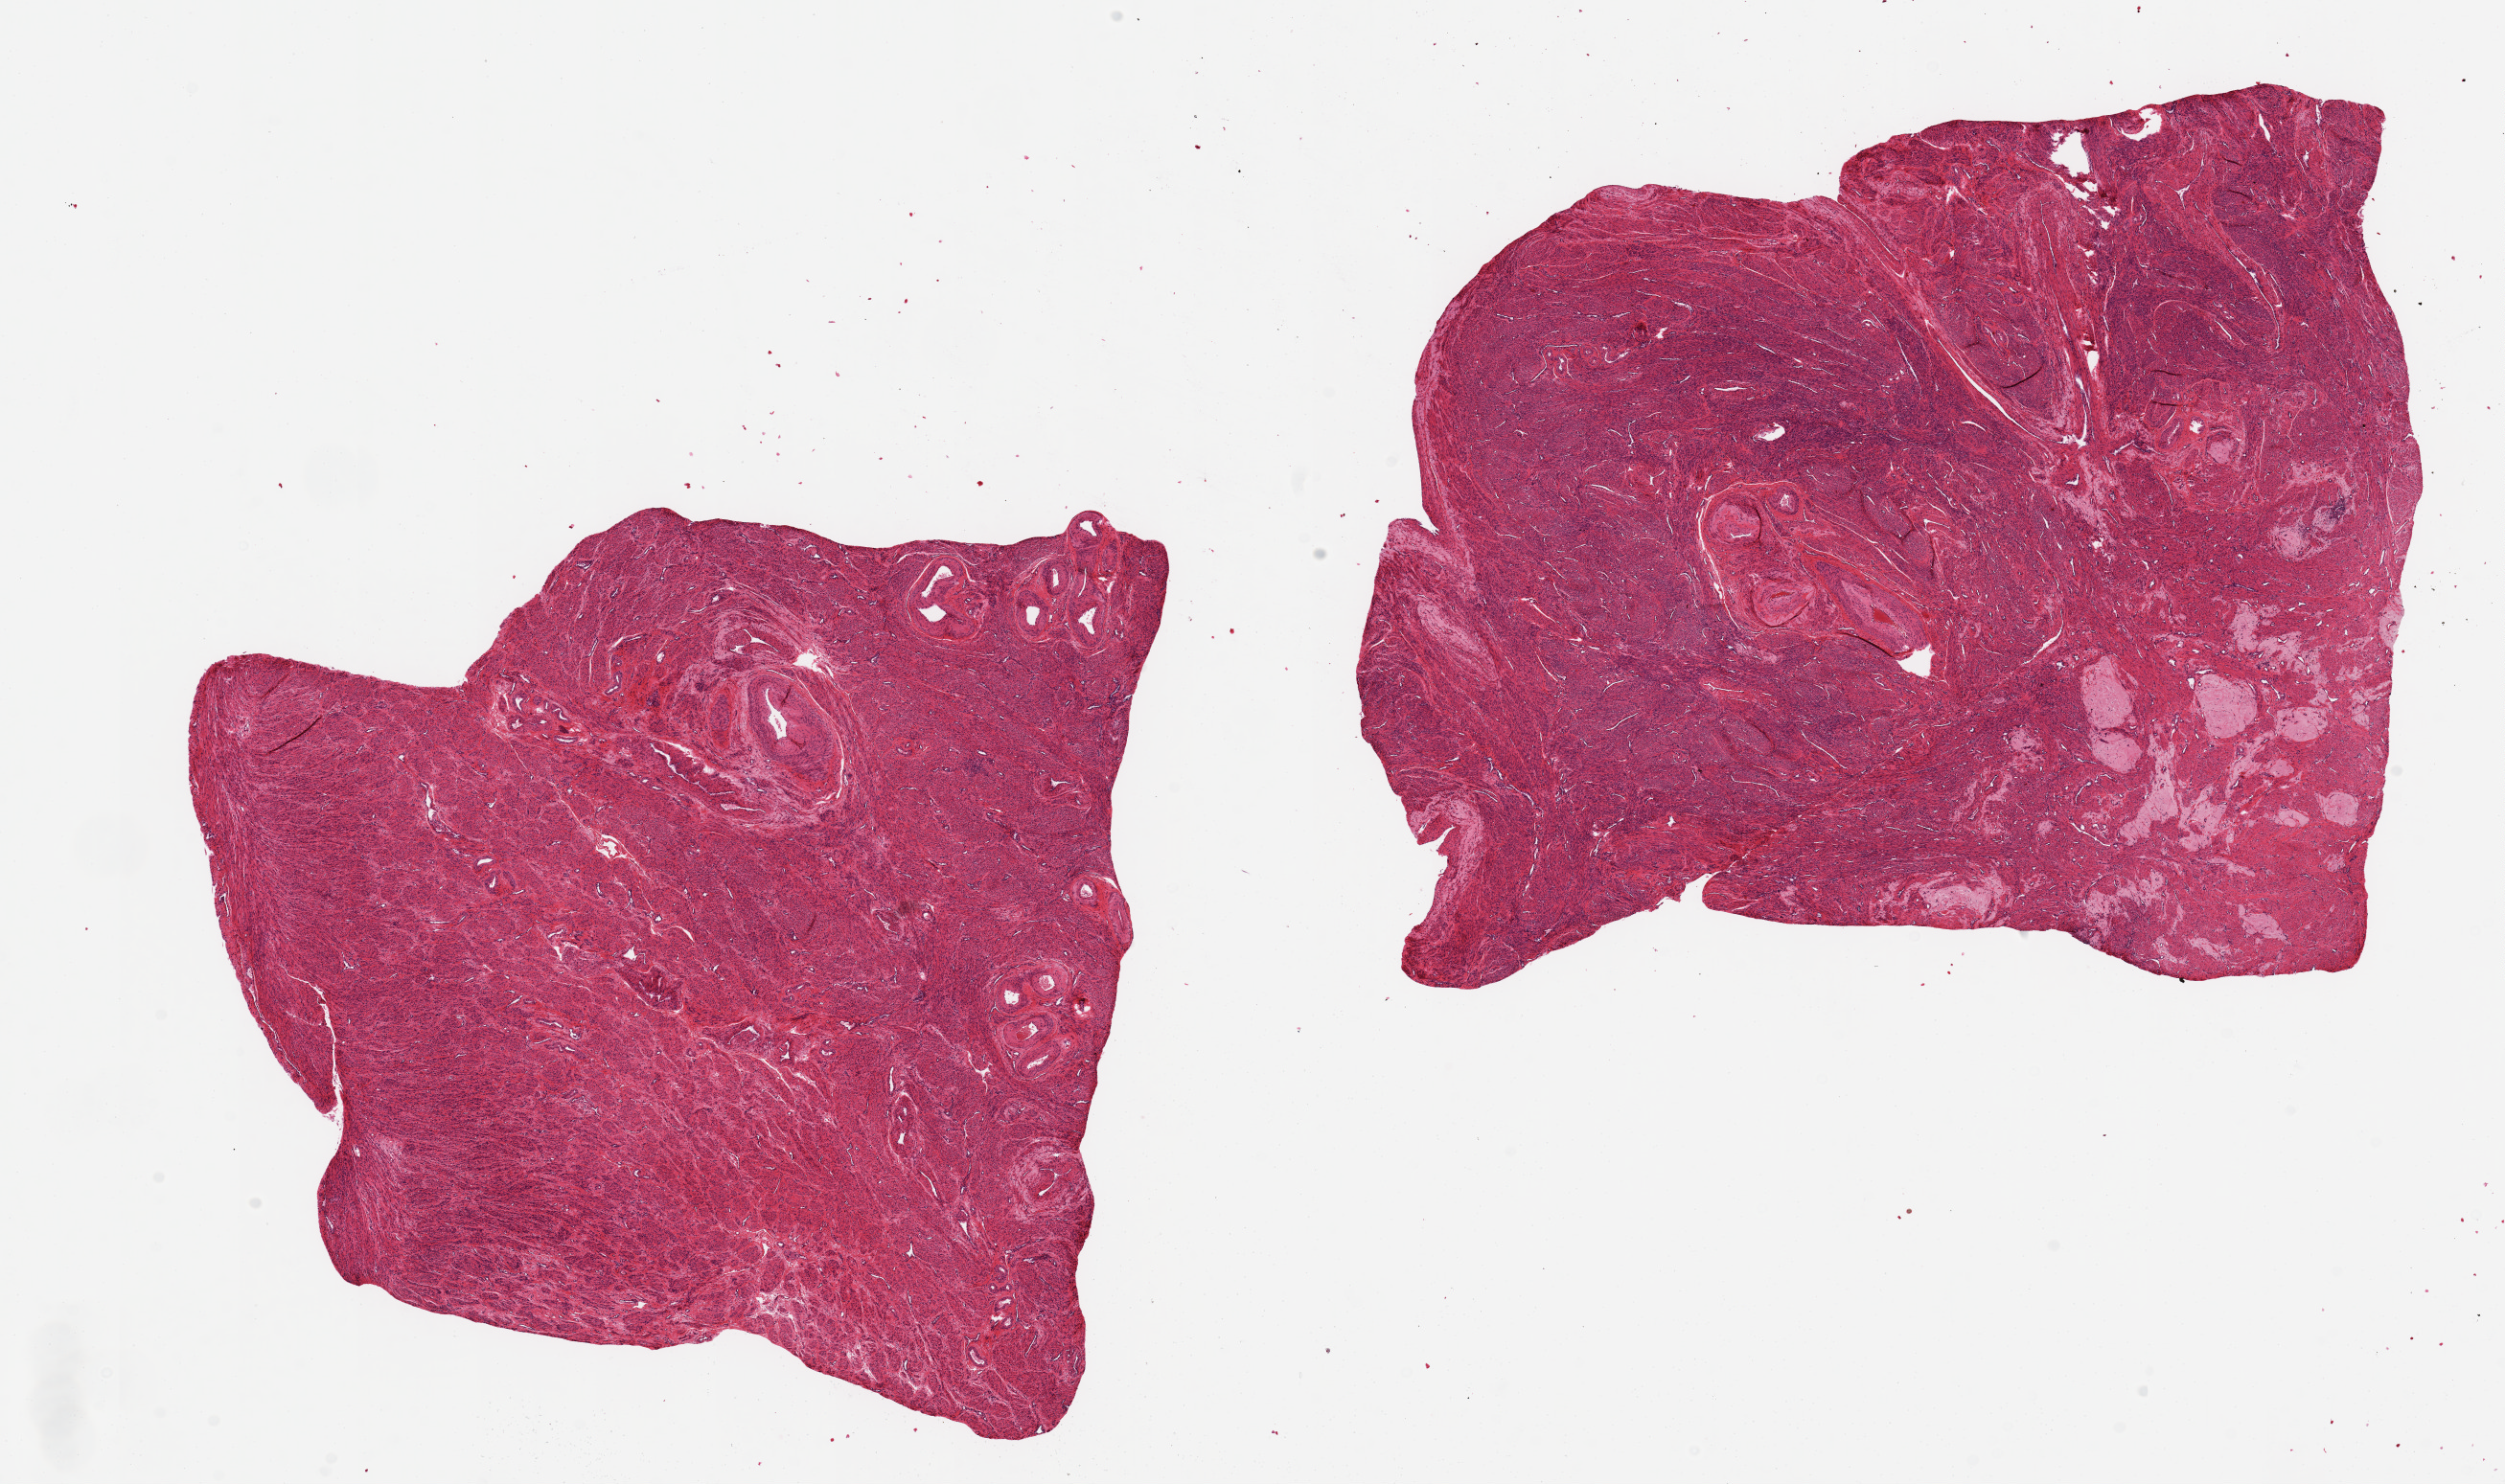
Digitized hematoxylin and eosin (H&E)-stained section — whole scanned area (about 20.7 x 12.3 mm, acquisition: 20x scan) shown as a low-resolution overview. PAXgene-fixed paraffin-embedded (PFPE) section. Target tissue: uterus. Tissue donor sample. Donor: female.
Pathologist's review note for this sample: 2 aliquots ~8x7mm; One has remote placental implantation site scarring; No endometrial glandular or stromal tissue is evident.